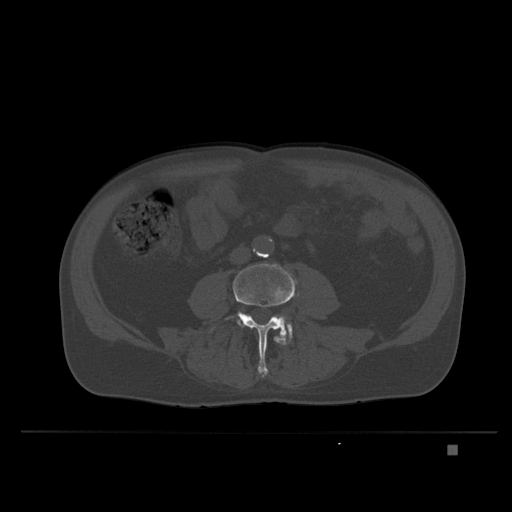
CT including the spine, one axial slice; position 74 of 435 along the scan axis; bone window (W 1800 / L 400 HU); 1.5 mm slice thickness; 512 × 512 image matrix, field of view 434 × 434 mm. Male patient, age 73 years. From the clinical record (not read from this slice): primary cancer: skin.
Annotated regions visible in this slice (semi-automatically segmented with operator editing):
- L4 vertebra: bounding box <211,263,295,377> (left, top, right, bottom; pixels)
- L5 vertebra: <249,315,292,344>